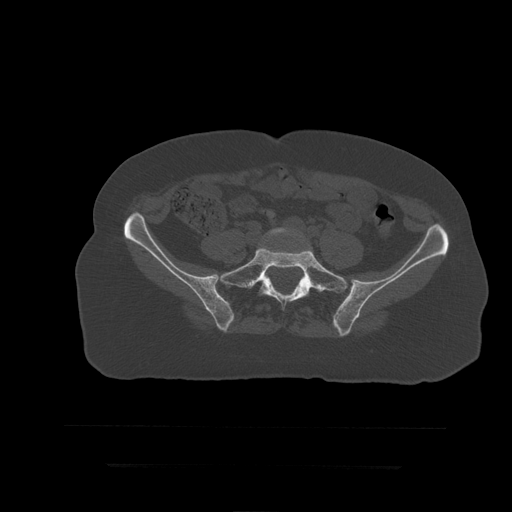
CT including the spine, one axial slice. Position 55 of 399 along the scan axis. Reconstruction kernel STANDARD. 120 kVp. Bone window (W 1800 / L 400 HU). 1.25 mm slice thickness. 512 × 512 image matrix, field of view 450 × 450 mm. Patient age 41 years. Case-level facts recorded for this patient, not image findings: primary cancer: breast.
Structures marked on this image (semi-automatically segmented with operator editing):
- L5 vertebra: box from (x=265, y=228) to (x=313, y=250) px